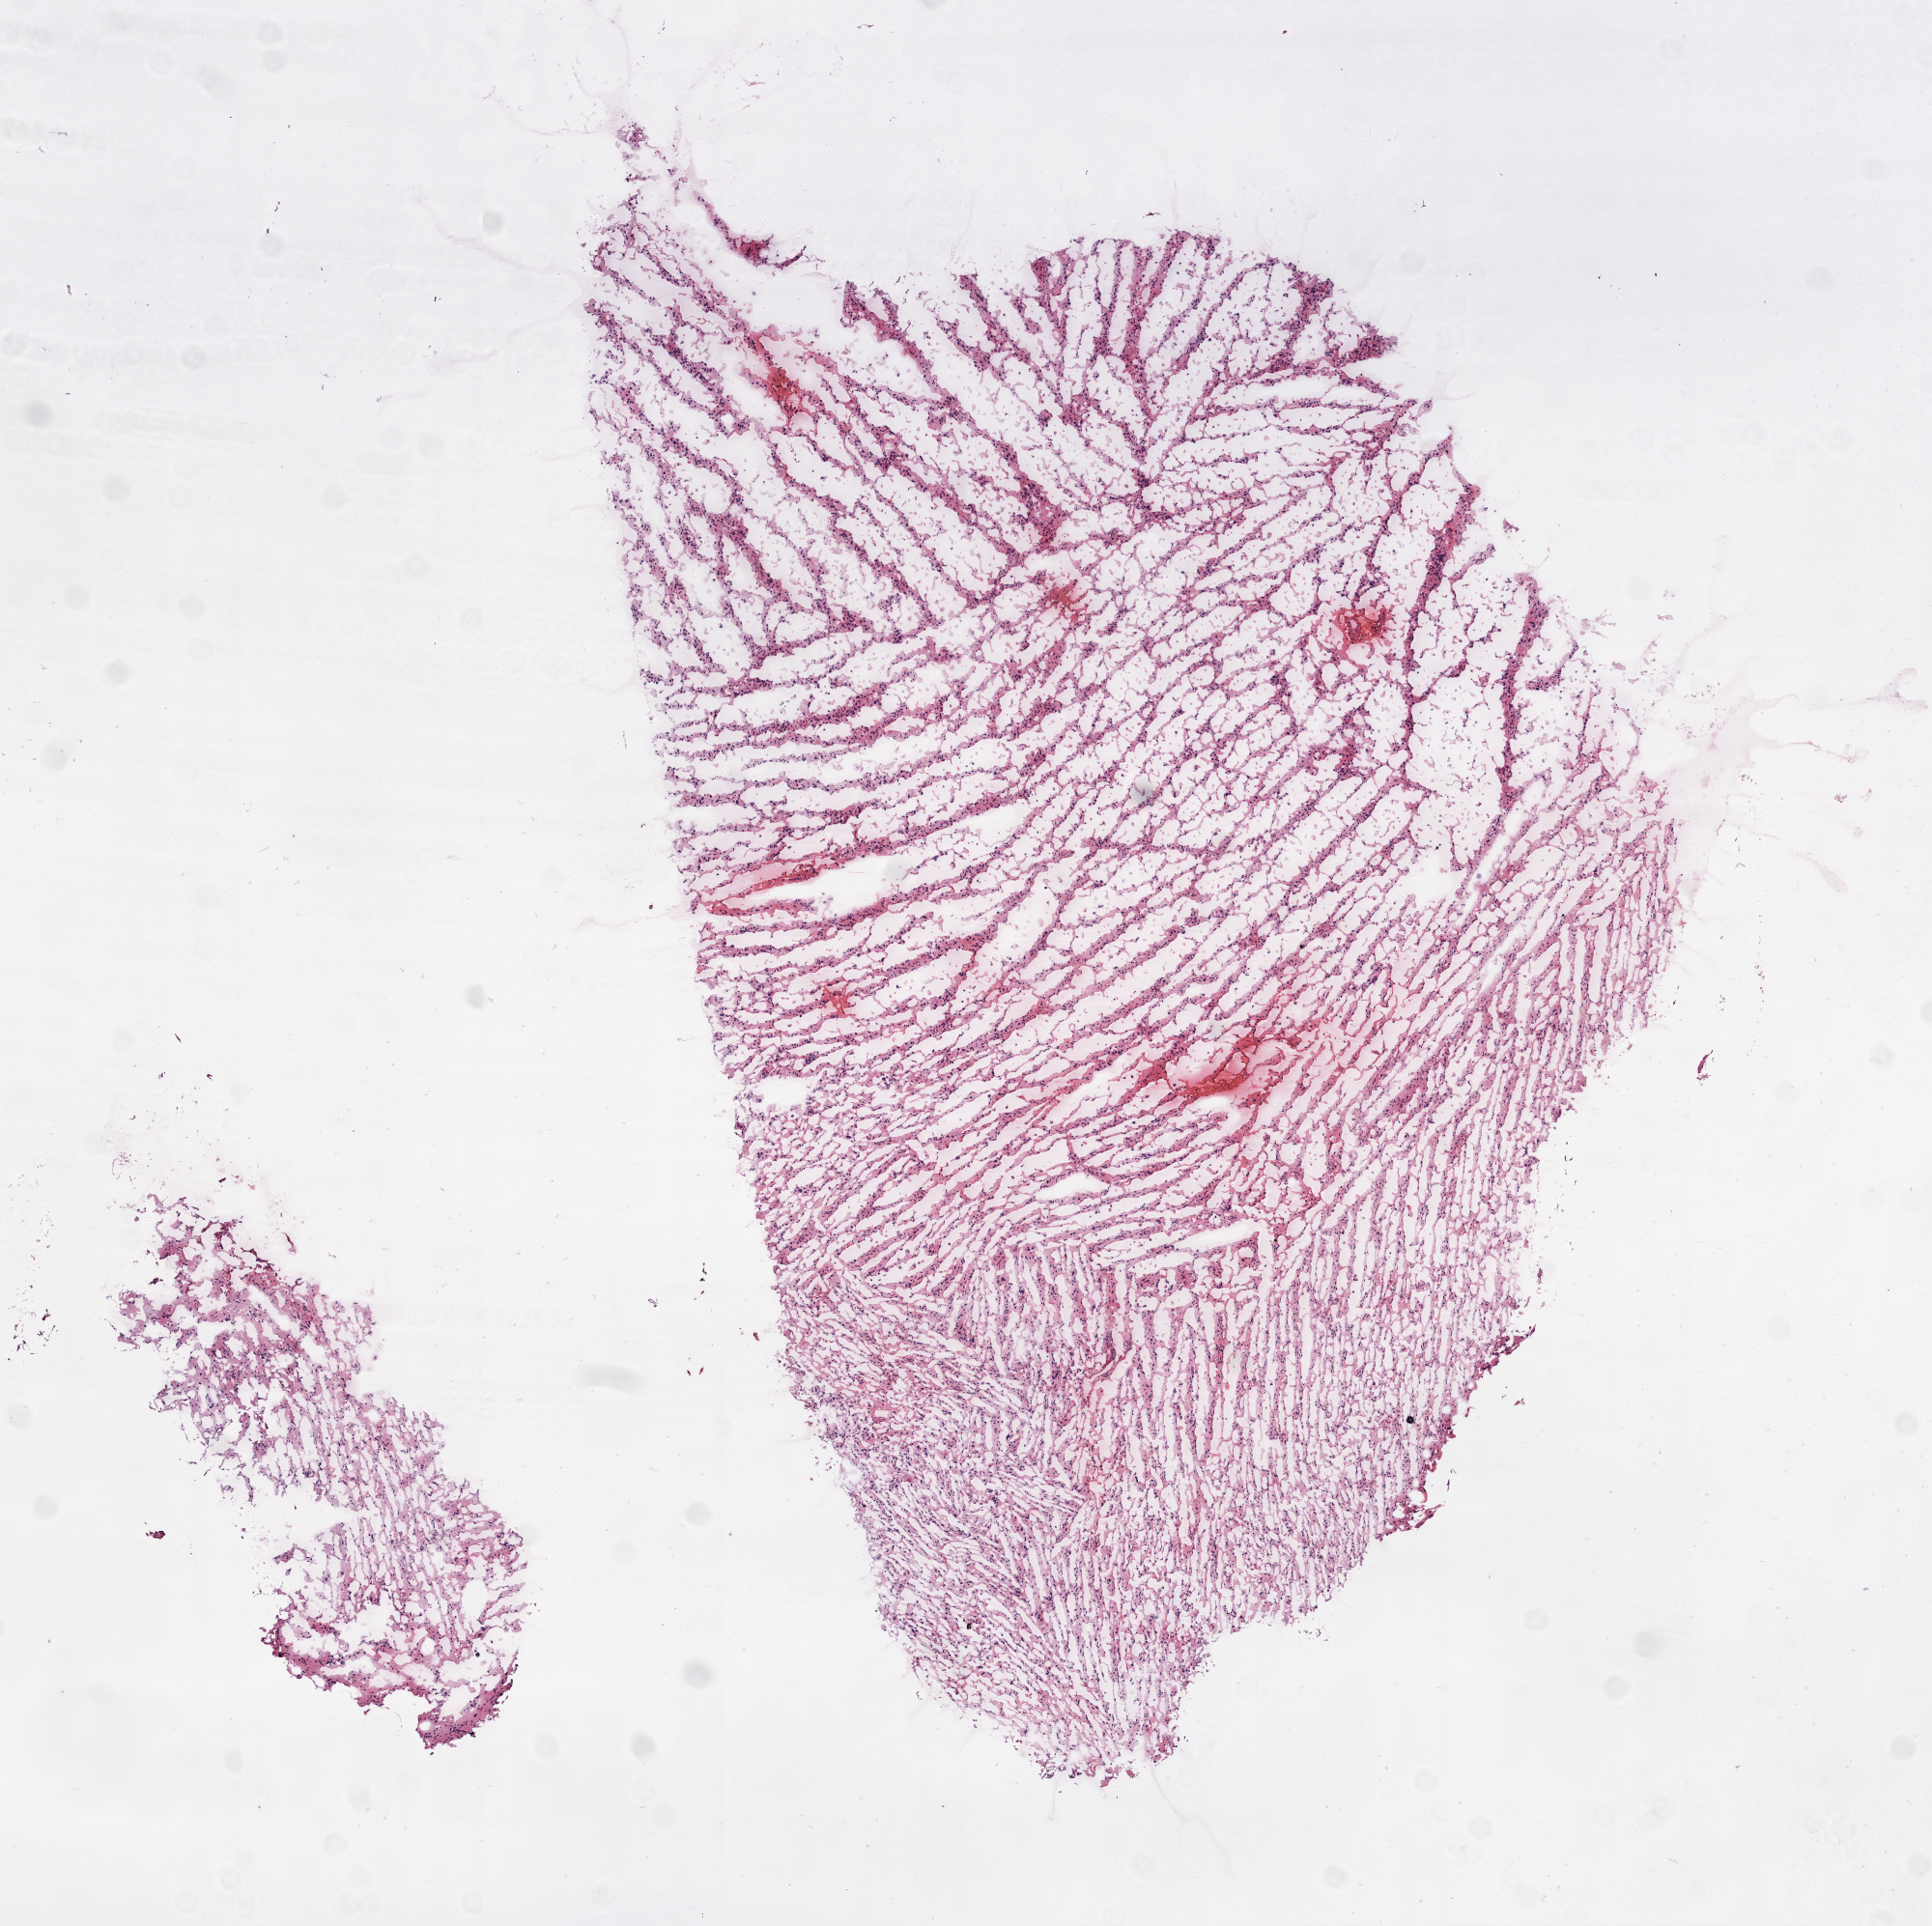
Whole-slide histology image, H&E-stained, shown as a low-resolution overview of the whole scanned area (about 8.0 x 8.0 mm); frozen section; sample: primary tumour, brain. Patient: male, age at initial diagnosis 37 years. Histologic grade: G3 (poorly differentiated). Pathologist review of this section (percent, as recorded): tumour cells 100%, tumour nuclei 70%, normal cells 0%, stromal cells 0%, necrosis 0%.
Diagnosis: Astrocytoma, anaplastic.